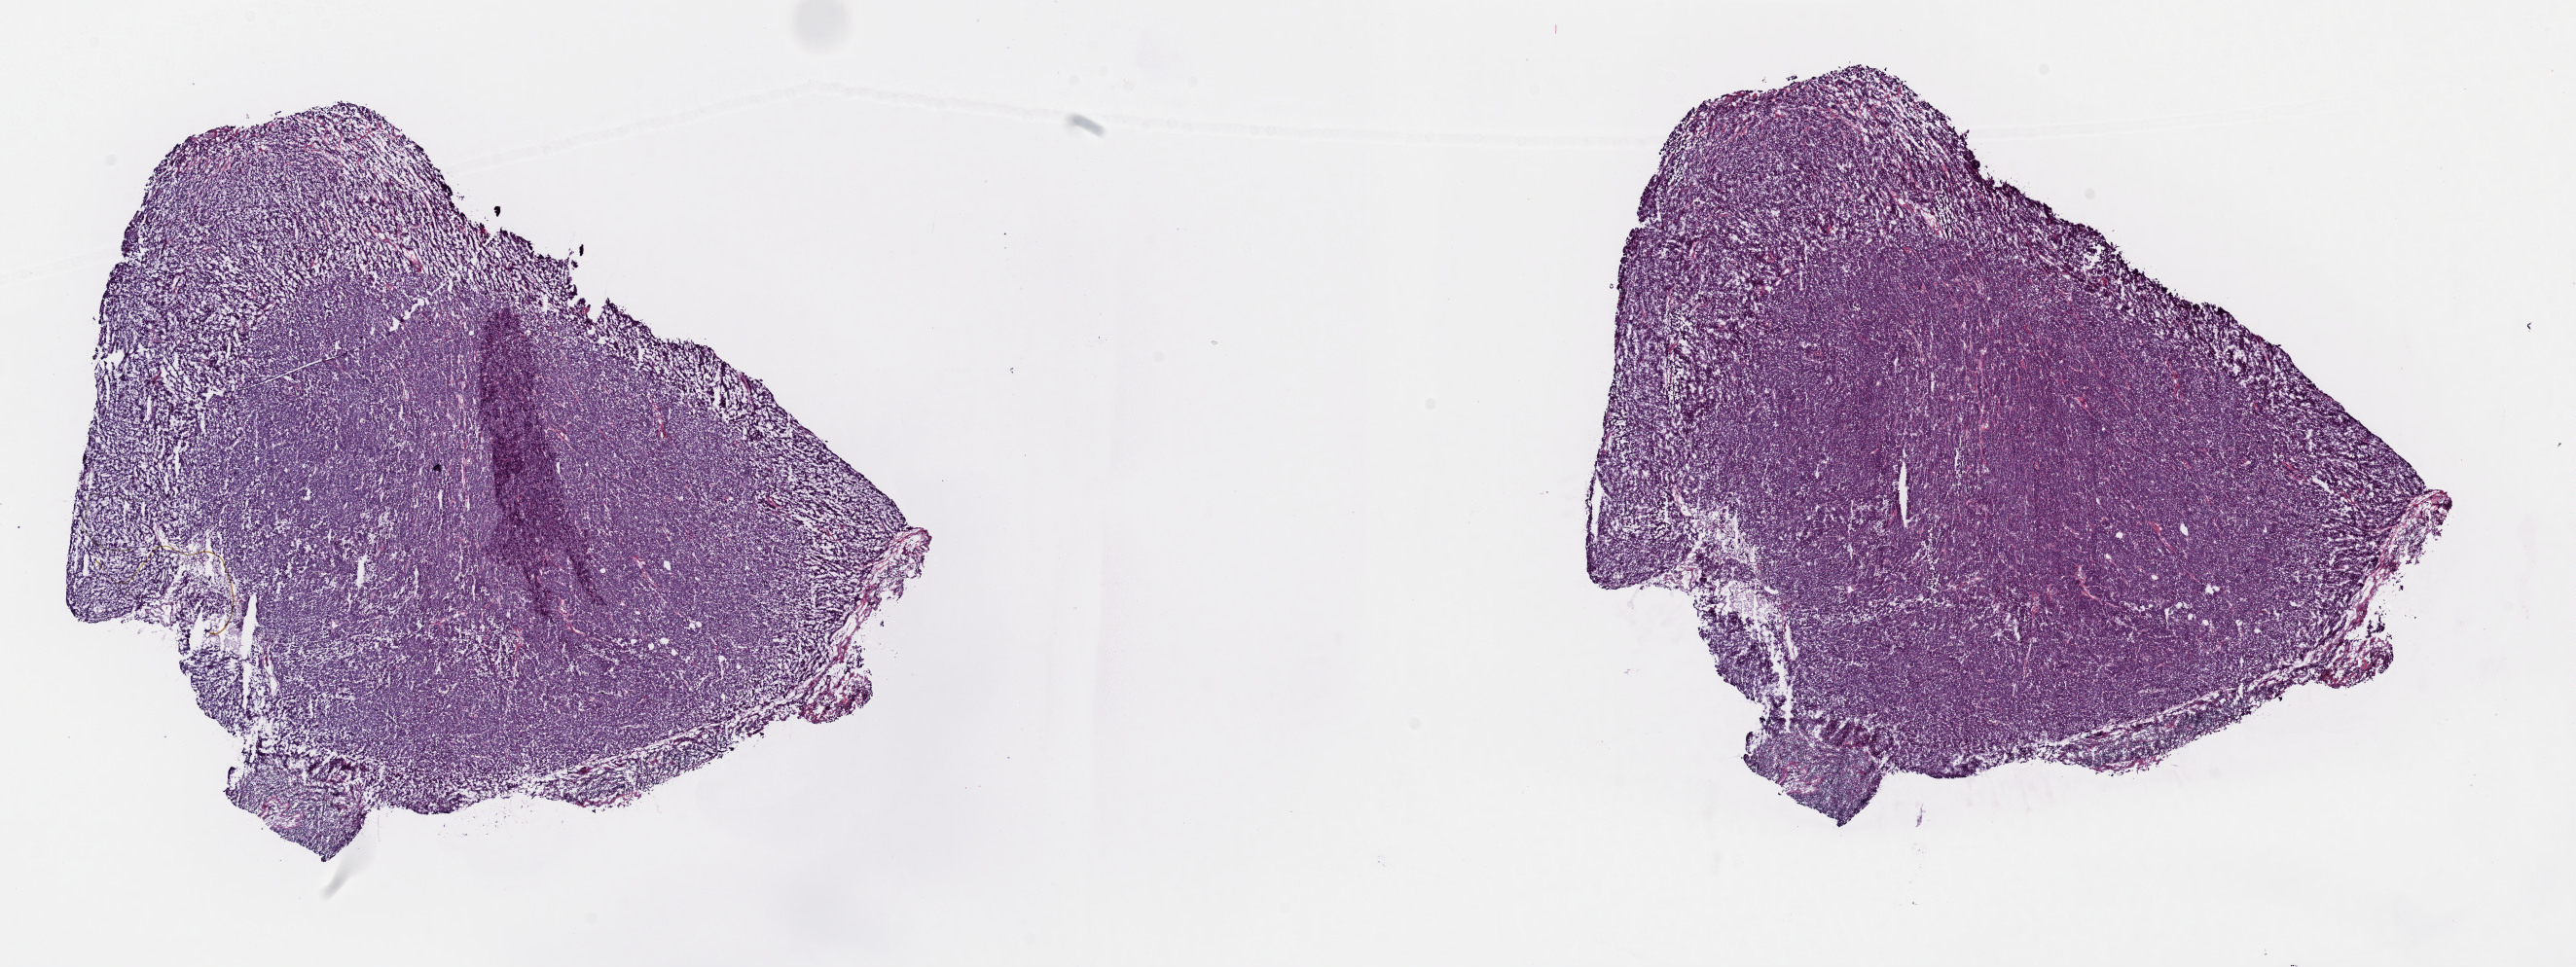
Whole-slide histology image, H&E-stained, low-resolution overview of the scanned area, about 20.9 x 7.9 mm (from a 40x scan), frozen section from the top of the tissue portion, metastatic tumour sample, sampled site: lymph node. Male patient; age at initial diagnosis 52 years.
This section: metastatic tumour tissue. Patient diagnosis: Malignant melanoma, NOS.